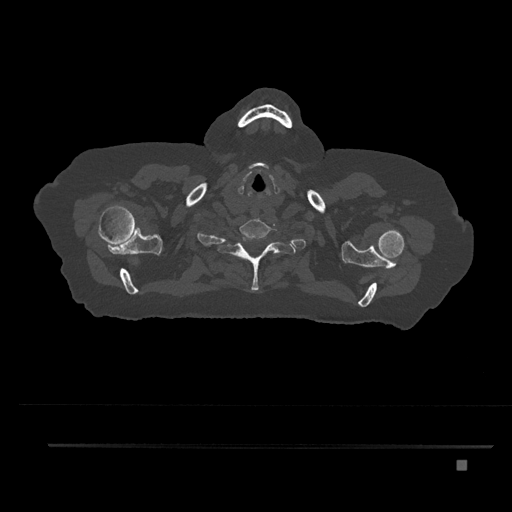
CT including the spine, one axial slice; position 706 of 797 along the scan axis; reconstruction kernel Br40s/3; bone window (W 1800 / L 400 HU); 512 × 512 image matrix. Female patient, age 76 years. From the clinical record (not read from this slice): primary cancer: lung; vertebrae with lytic lesions (as recorded): T11, L3.
Structures marked on this image (semi-automatically segmented with operator editing):
- T1 vertebra: box from (x=224, y=234) to (x=283, y=292) px